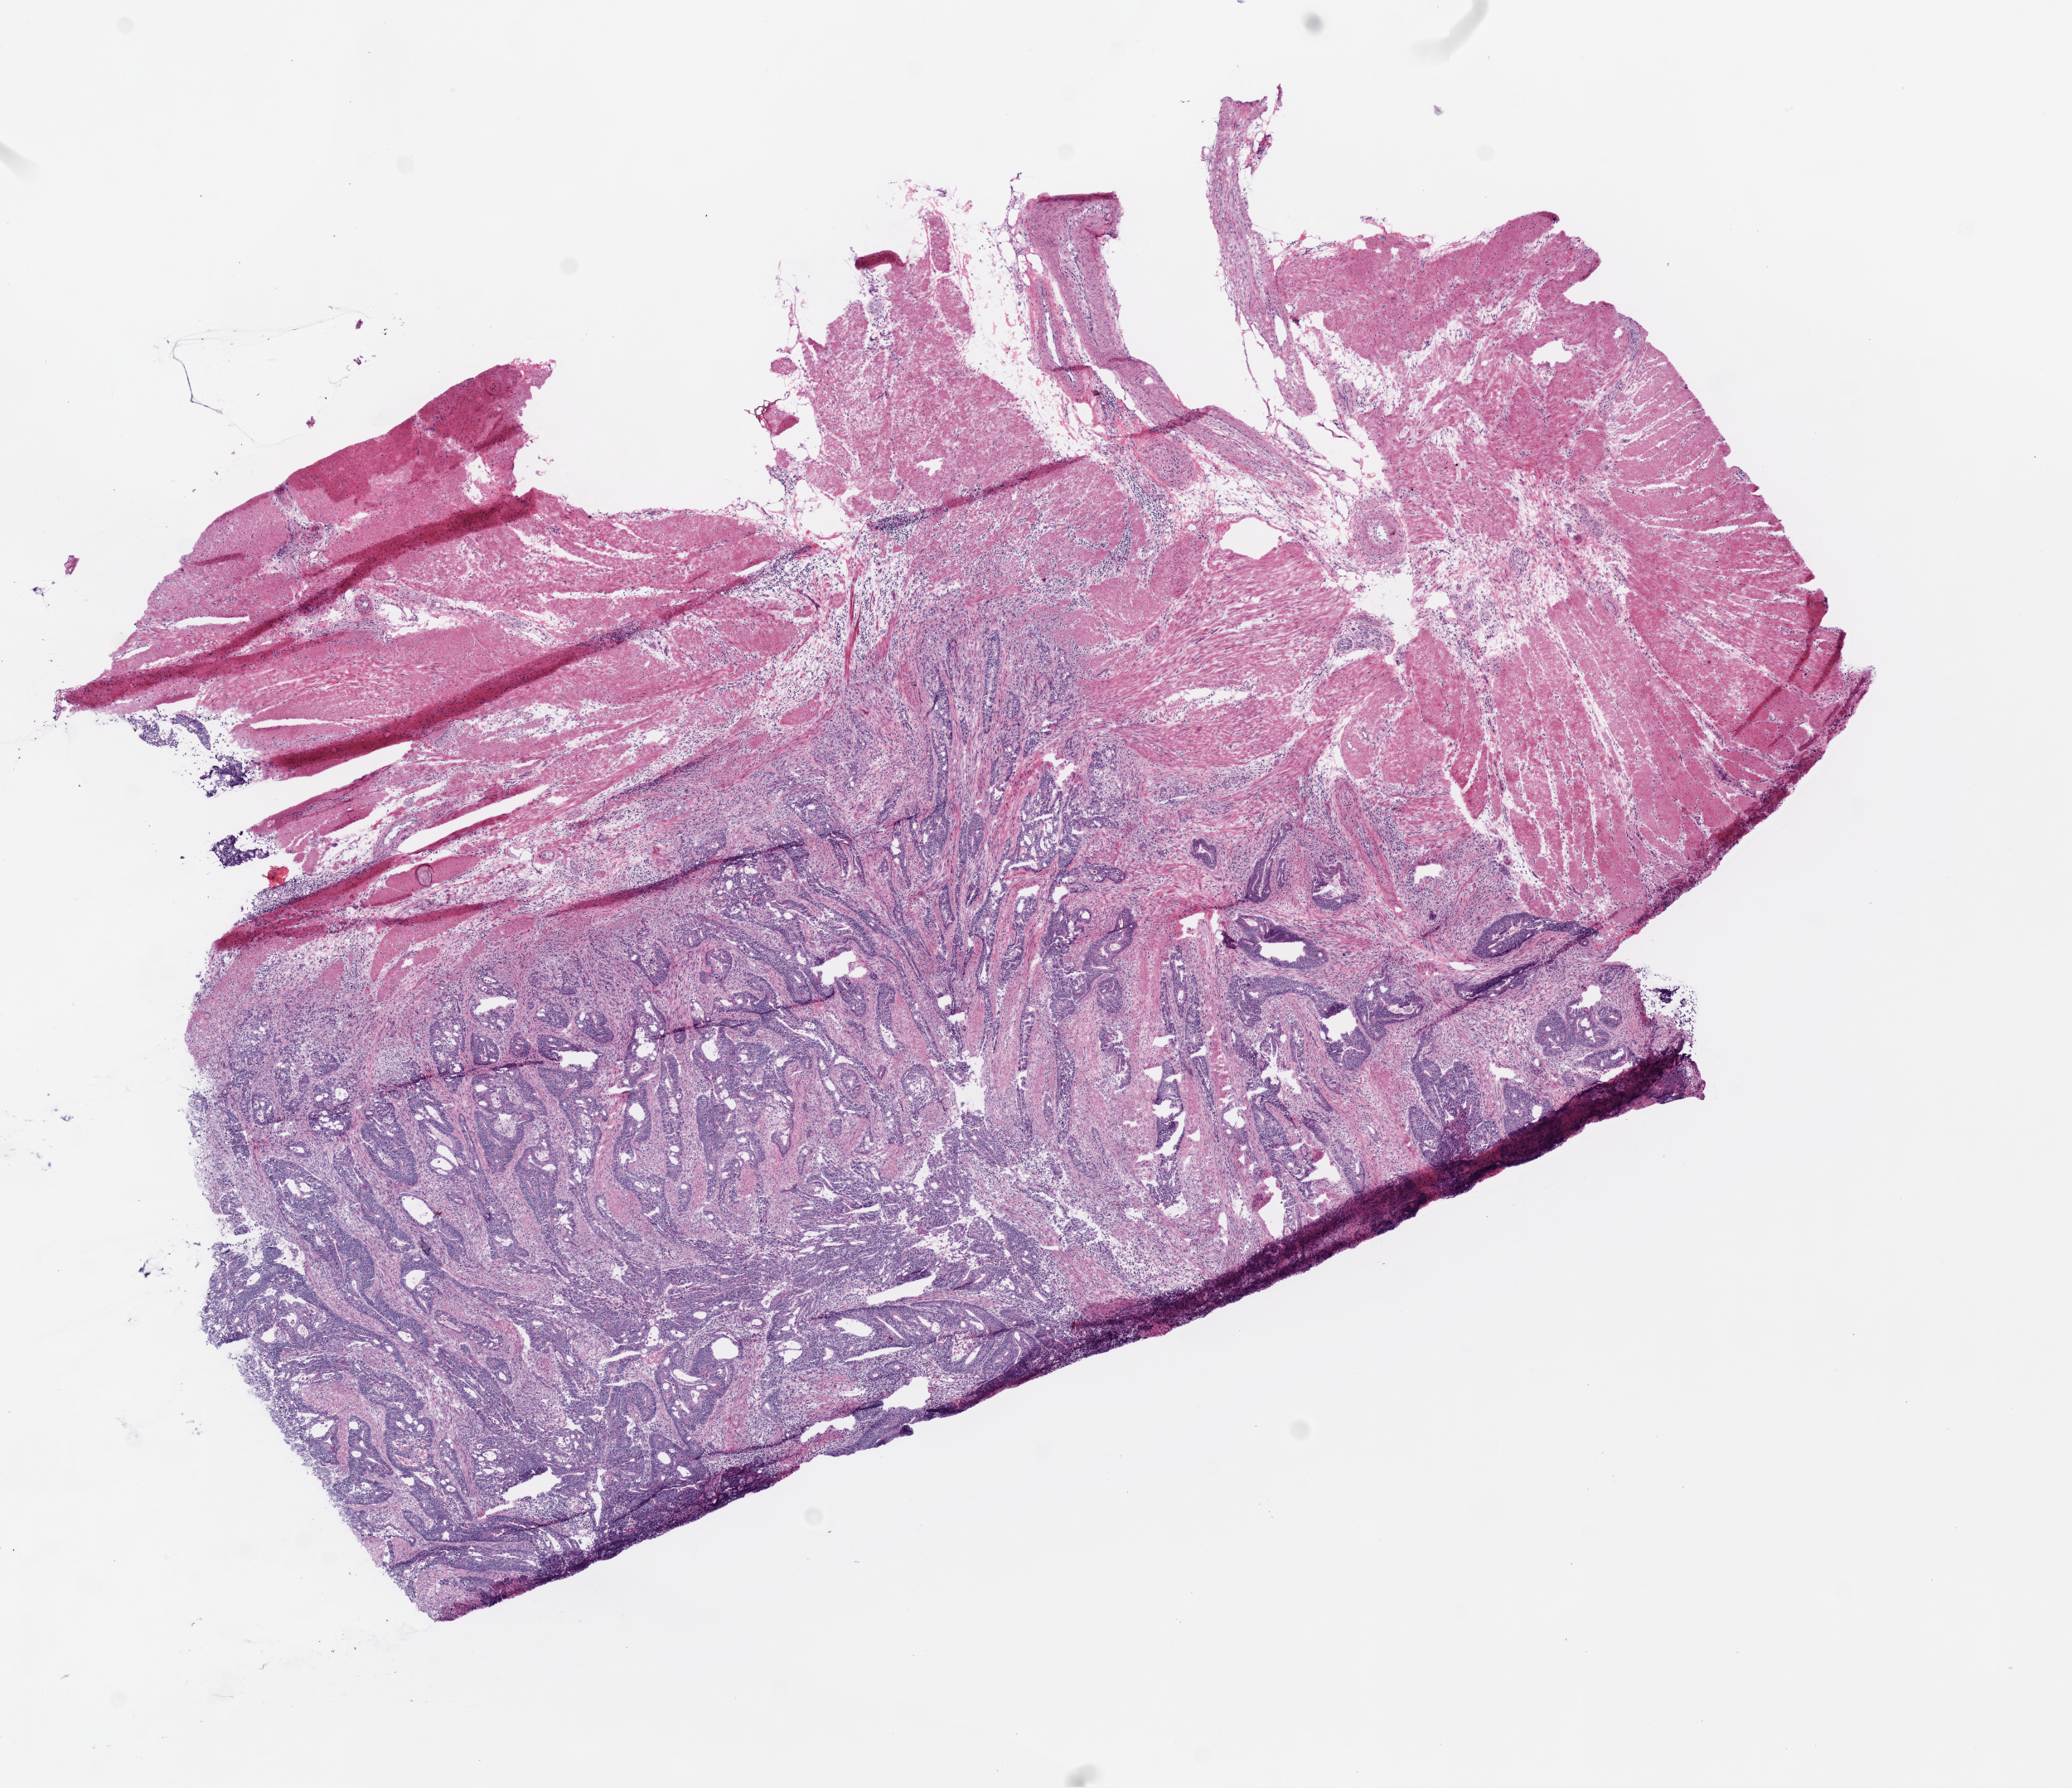
H&E whole-slide image — shown as a low-resolution overview of the whole scanned area (about 10.0 x 8.7 mm, from a 20x scan). Frozen section from the bottom of the tissue portion. Primary tumour sample from the colon. Female, age 75 years at initial diagnosis. Pathologist review of this section (percent, as recorded): tumour cells 58%, tumour nuclei 75%, normal cells 30%, stromal cells 10%, necrosis 2%.
Histologic diagnosis: Adenocarcinoma, NOS. AJCC pathologic stage: I.